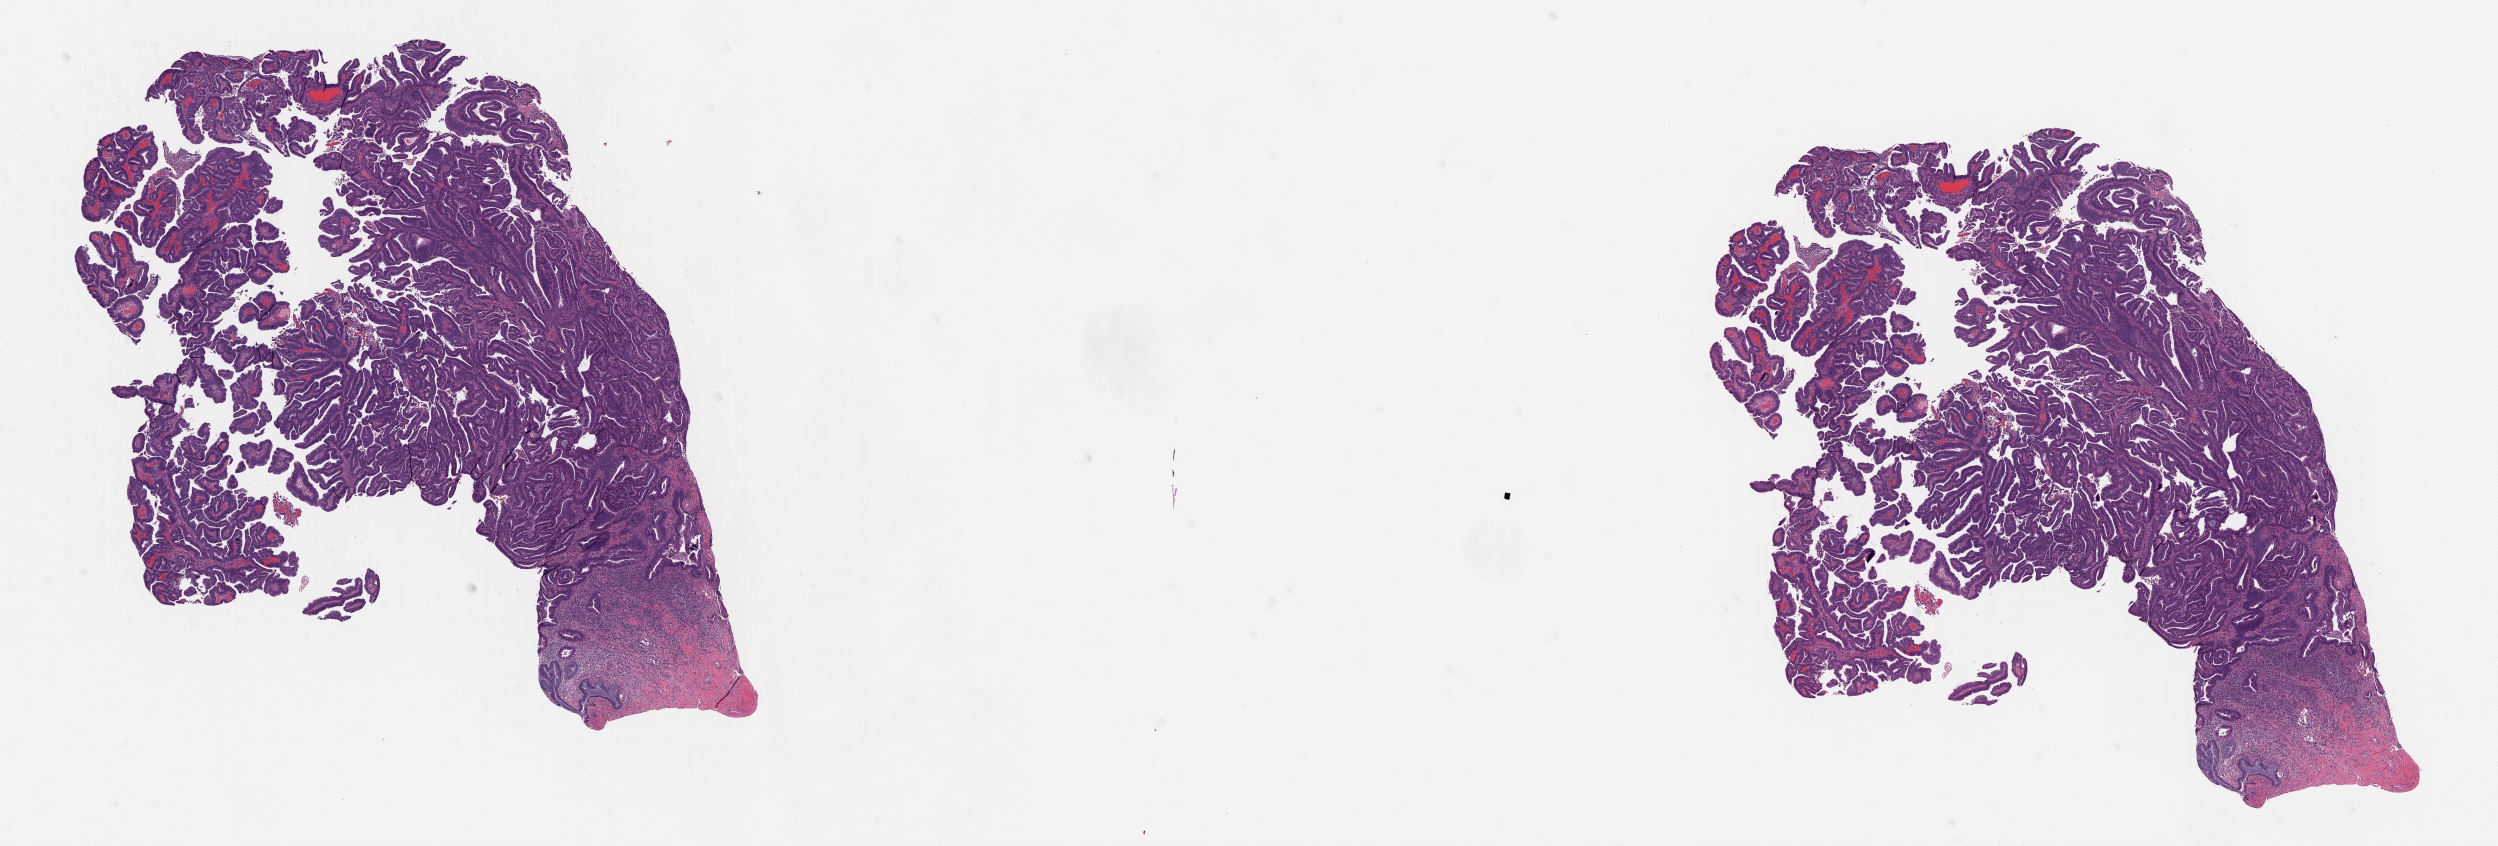
Whole-slide histology image, H&E-stained, shown as a low-resolution overview of the whole scanned area (about 20.0 x 6.8 mm, slide scanned at 20x); formalin-fixed paraffin-embedded (FFPE) diagnostic section; sample: primary tumour, cervix. Female, age 25 years at initial diagnosis. Histologic grade: GX (grade cannot be assessed).
Lymph nodes positive (case pathology): 0 of 12 examined. FIGO stage: IB1. Pathologic diagnosis: Adenocarcinoma, NOS (cervix uteri).